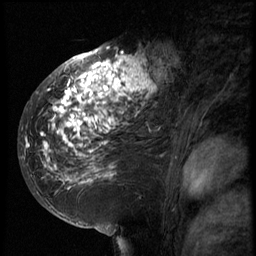
Breast MRI (dynamic contrast-enhanced), one sagittal slice. Slice 38 of 66 in the series (ordered by position). 3 images stored at this slice position (order not interpretable as contrast timing). 1.5 T. TE 4.2 ms, TR 8.9 ms. 256 × 256 image matrix, field of view 200 × 200 mm. Female patient, age 39 years. Case-level facts recorded for this patient, not image findings: setting: breast cancer imaged before/during neoadjuvant chemotherapy; receptor status: HER2-positive.
Structures marked on this image (semi-automatically segmented with operator editing):
- analysis volume of interest (the breast-tissue region the enhancement analysis was run in; not a lesion): box from (x=29, y=44) to (x=166, y=196) px
- tumour enhancement mask (voxels above the 140 % enhancement threshold inside the analysis volume of interest): (x=29, y=46)–(x=166, y=188)